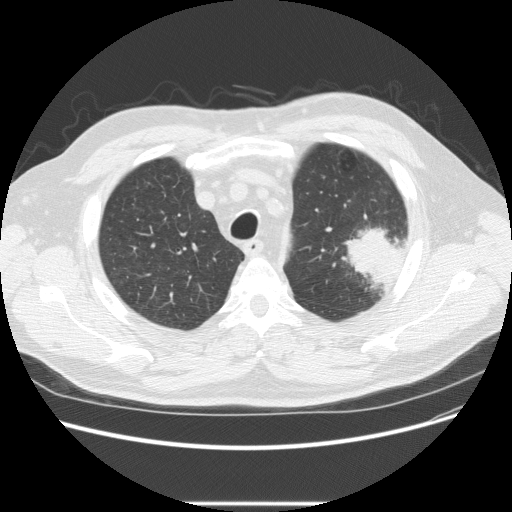
Low-dose screening chest CT, one axial slice. Slice 182 of 233 in the series (ordered by position). Lung window (W 1500 / L -600 HU). 512 × 512 image matrix, field of view 380 × 380 mm.
Outlined on this slice (expert manual segmentation):
- lesion 1 (tumor, upper lobe of left lung): bounding box (x1, y1, x2, y2) in pixels: (341, 224, 401, 292)